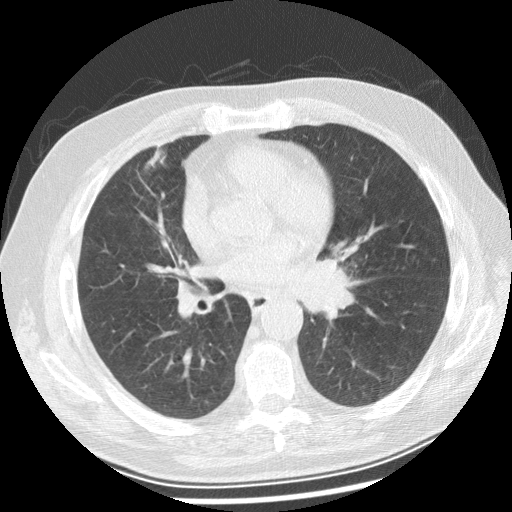
Low-dose screening chest CT, one axial slice; position 128 of 250 along the scan axis; lung window (W 1500 / L -600 HU); 2.5 mm slice thickness; 512 × 512 image matrix, field of view 360 × 360 mm.
Outlined on this slice (manually delineated by an expert):
- lesion 1 (tumor, left main bronchus): bounding box [x1, y1, x2, y2] px = [298, 258, 356, 319]